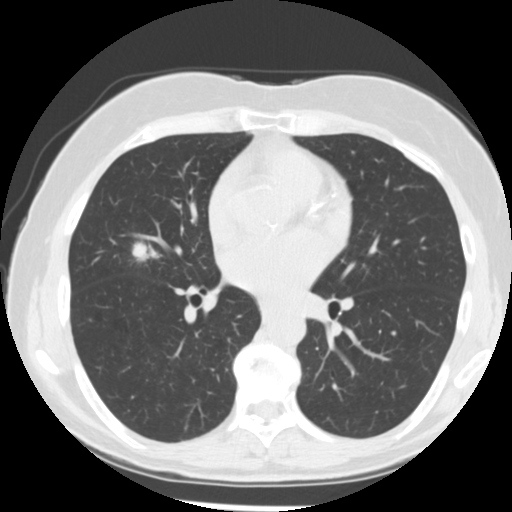
Low-dose screening chest CT, one axial slice. Reconstruction kernel STANDARD. 120 kVp. Lung window (W 1500 / L -600 HU). 2.5 mm slice thickness. 512 × 512 image matrix, field of view 320 × 320 mm.
Structures marked on this image (manually delineated by an expert):
- lesion 1 (tumor, middle lobe of right lung): bounding box [x1, y1, x2, y2] px = [132, 241, 159, 261]